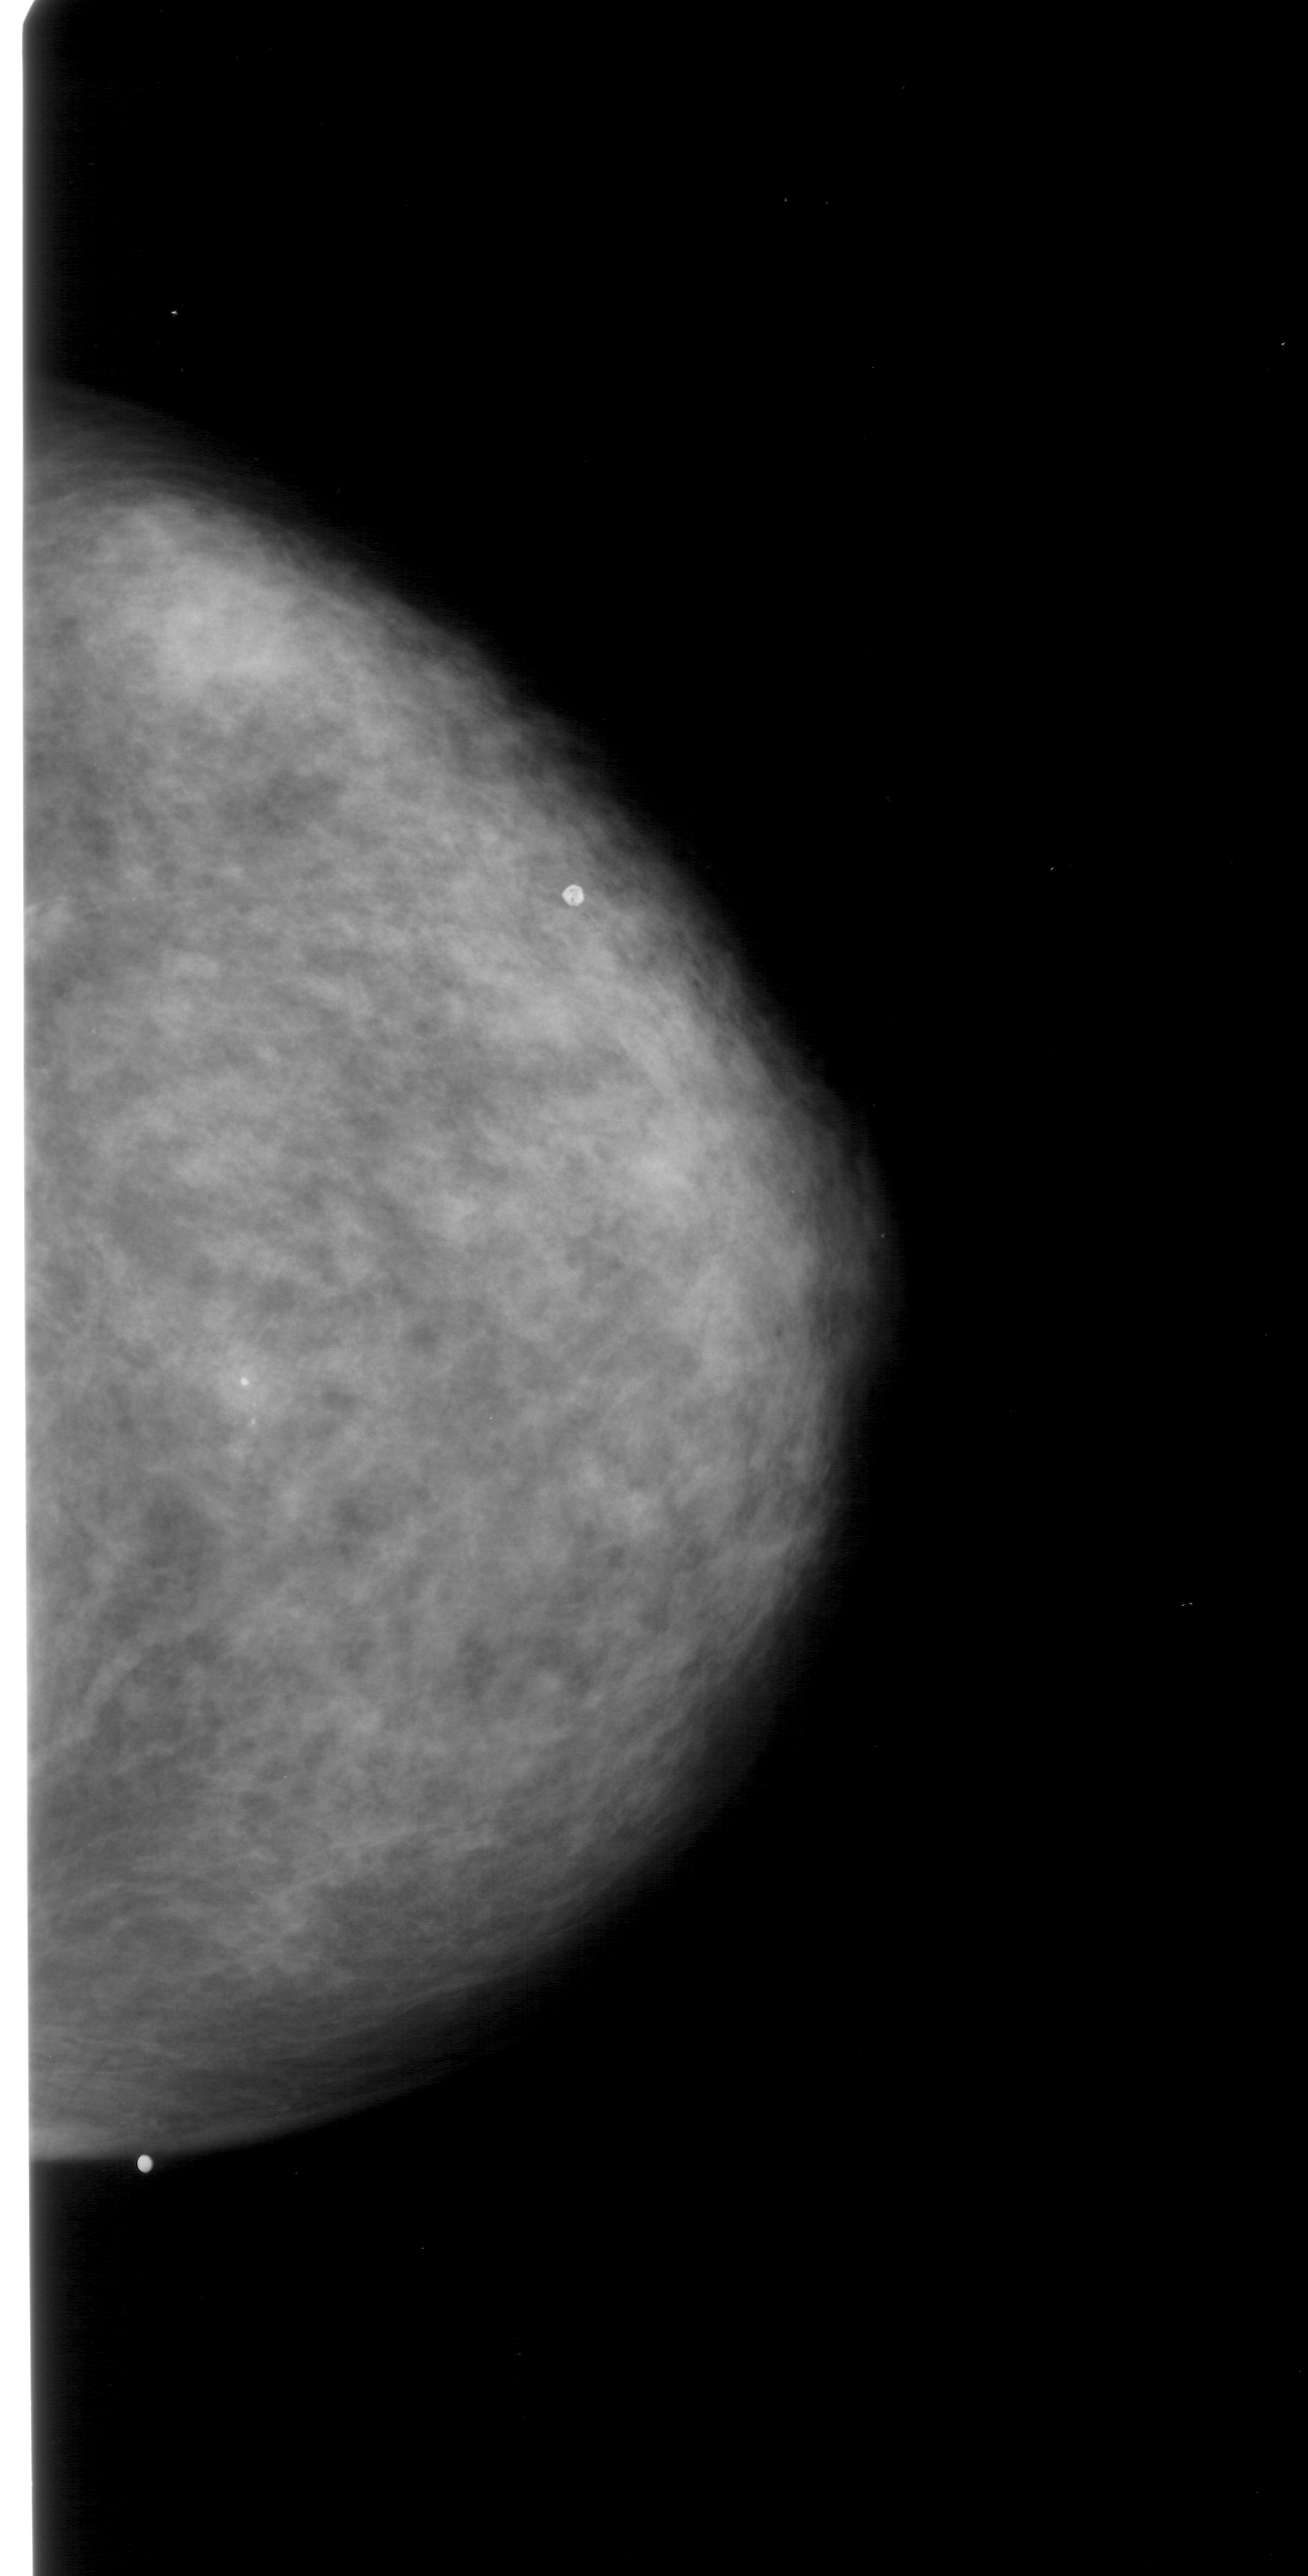
Scanned film-screen mammogram. Right breast. CC view. BI-RADS breast density category 3 (scale 1–4). 1308 × 2576 image matrix.
Marked abnormalities (boxes around the expert regions of interest):
- calcifications, morphology pleomorphic, distribution clustered; BI-RADS assessment category 4; subtlety rating 2 on a 1 (subtle) to 5 (obvious) scale; pathology (as recorded): malignant: bounding box [x1, y1, x2, y2] px = [227, 1337, 305, 1432]